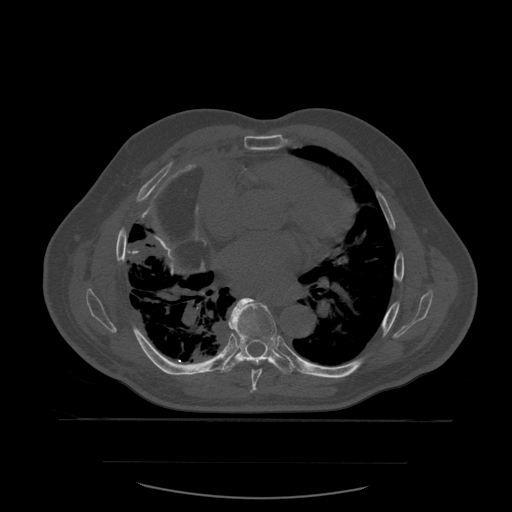
CT including the spine, one axial slice; position 370 of 590 along the scan axis; bone window (W 1800 / L 400 HU); 1.25 mm slice thickness; 512 × 512 image matrix, field of view 479 × 479 mm. Patient age 71 years. Case-level facts recorded for this patient, not image findings: primary cancer: lung; vertebrae with lytic lesions (as recorded): T1, T2, L5, S1.
Outlined on this slice (semi-automatically segmented with operator editing):
- T7 vertebra: bounding box <248,299,263,393> (left, top, right, bottom; pixels)
- T8 vertebra: <222,298,294,375>